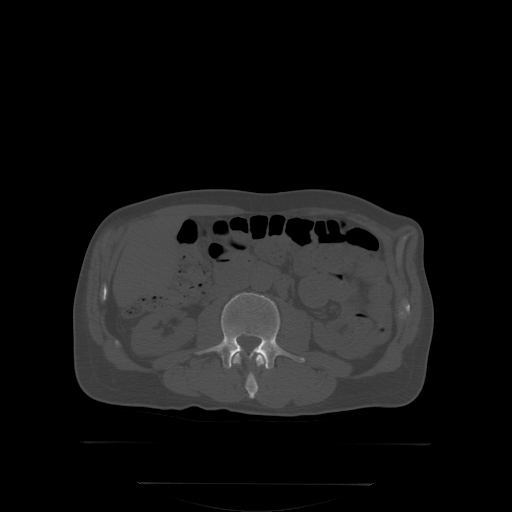
CT including the spine, one axial slice; position 127 of 350 along the scan axis; bone window (W 1800 / L 400 HU); 2.5 mm slice thickness; 512 × 512 image matrix, field of view 500 × 500 mm. Patient: male, 58 years. Case-level facts recorded for this patient, not image findings: primary cancer: prostate.
Structures marked on this image (semi-automatic segmentation, software-assisted and operator-edited):
- L2 vertebra: bounding box (x1, y1, x2, y2) in pixels: (232, 350, 267, 399)
- L3 vertebra: (194, 292, 306, 368)